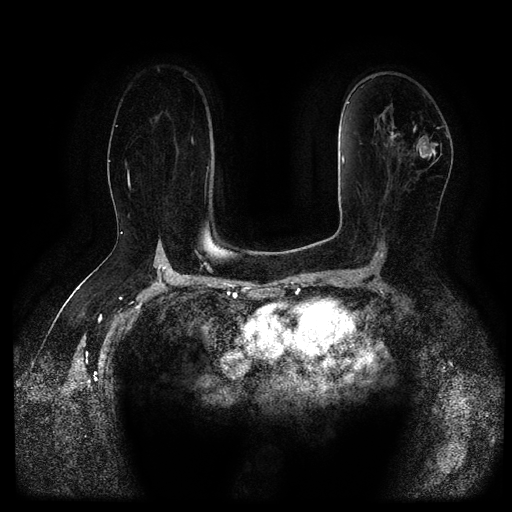
Breast MRI (dynamic contrast-enhanced, multi-phase), one axial slice. Dynamic contrast-enhanced series, time point 2 of 5 at this slice position (early post-contrast). 1.5 T. TE 2.6 ms, TR 5.3 ms. 2 mm slice thickness. 512 × 512 image matrix. Patient: female, 67 years.
Outlined on this slice (semi-automatic segmentation, software-assisted and operator-edited):
- breast lesion (labelled 'tumour' in the annotation; benign lesions carry a separate 'benign' label): bounding box <389,125,401,147> (left, top, right, bottom; pixels)